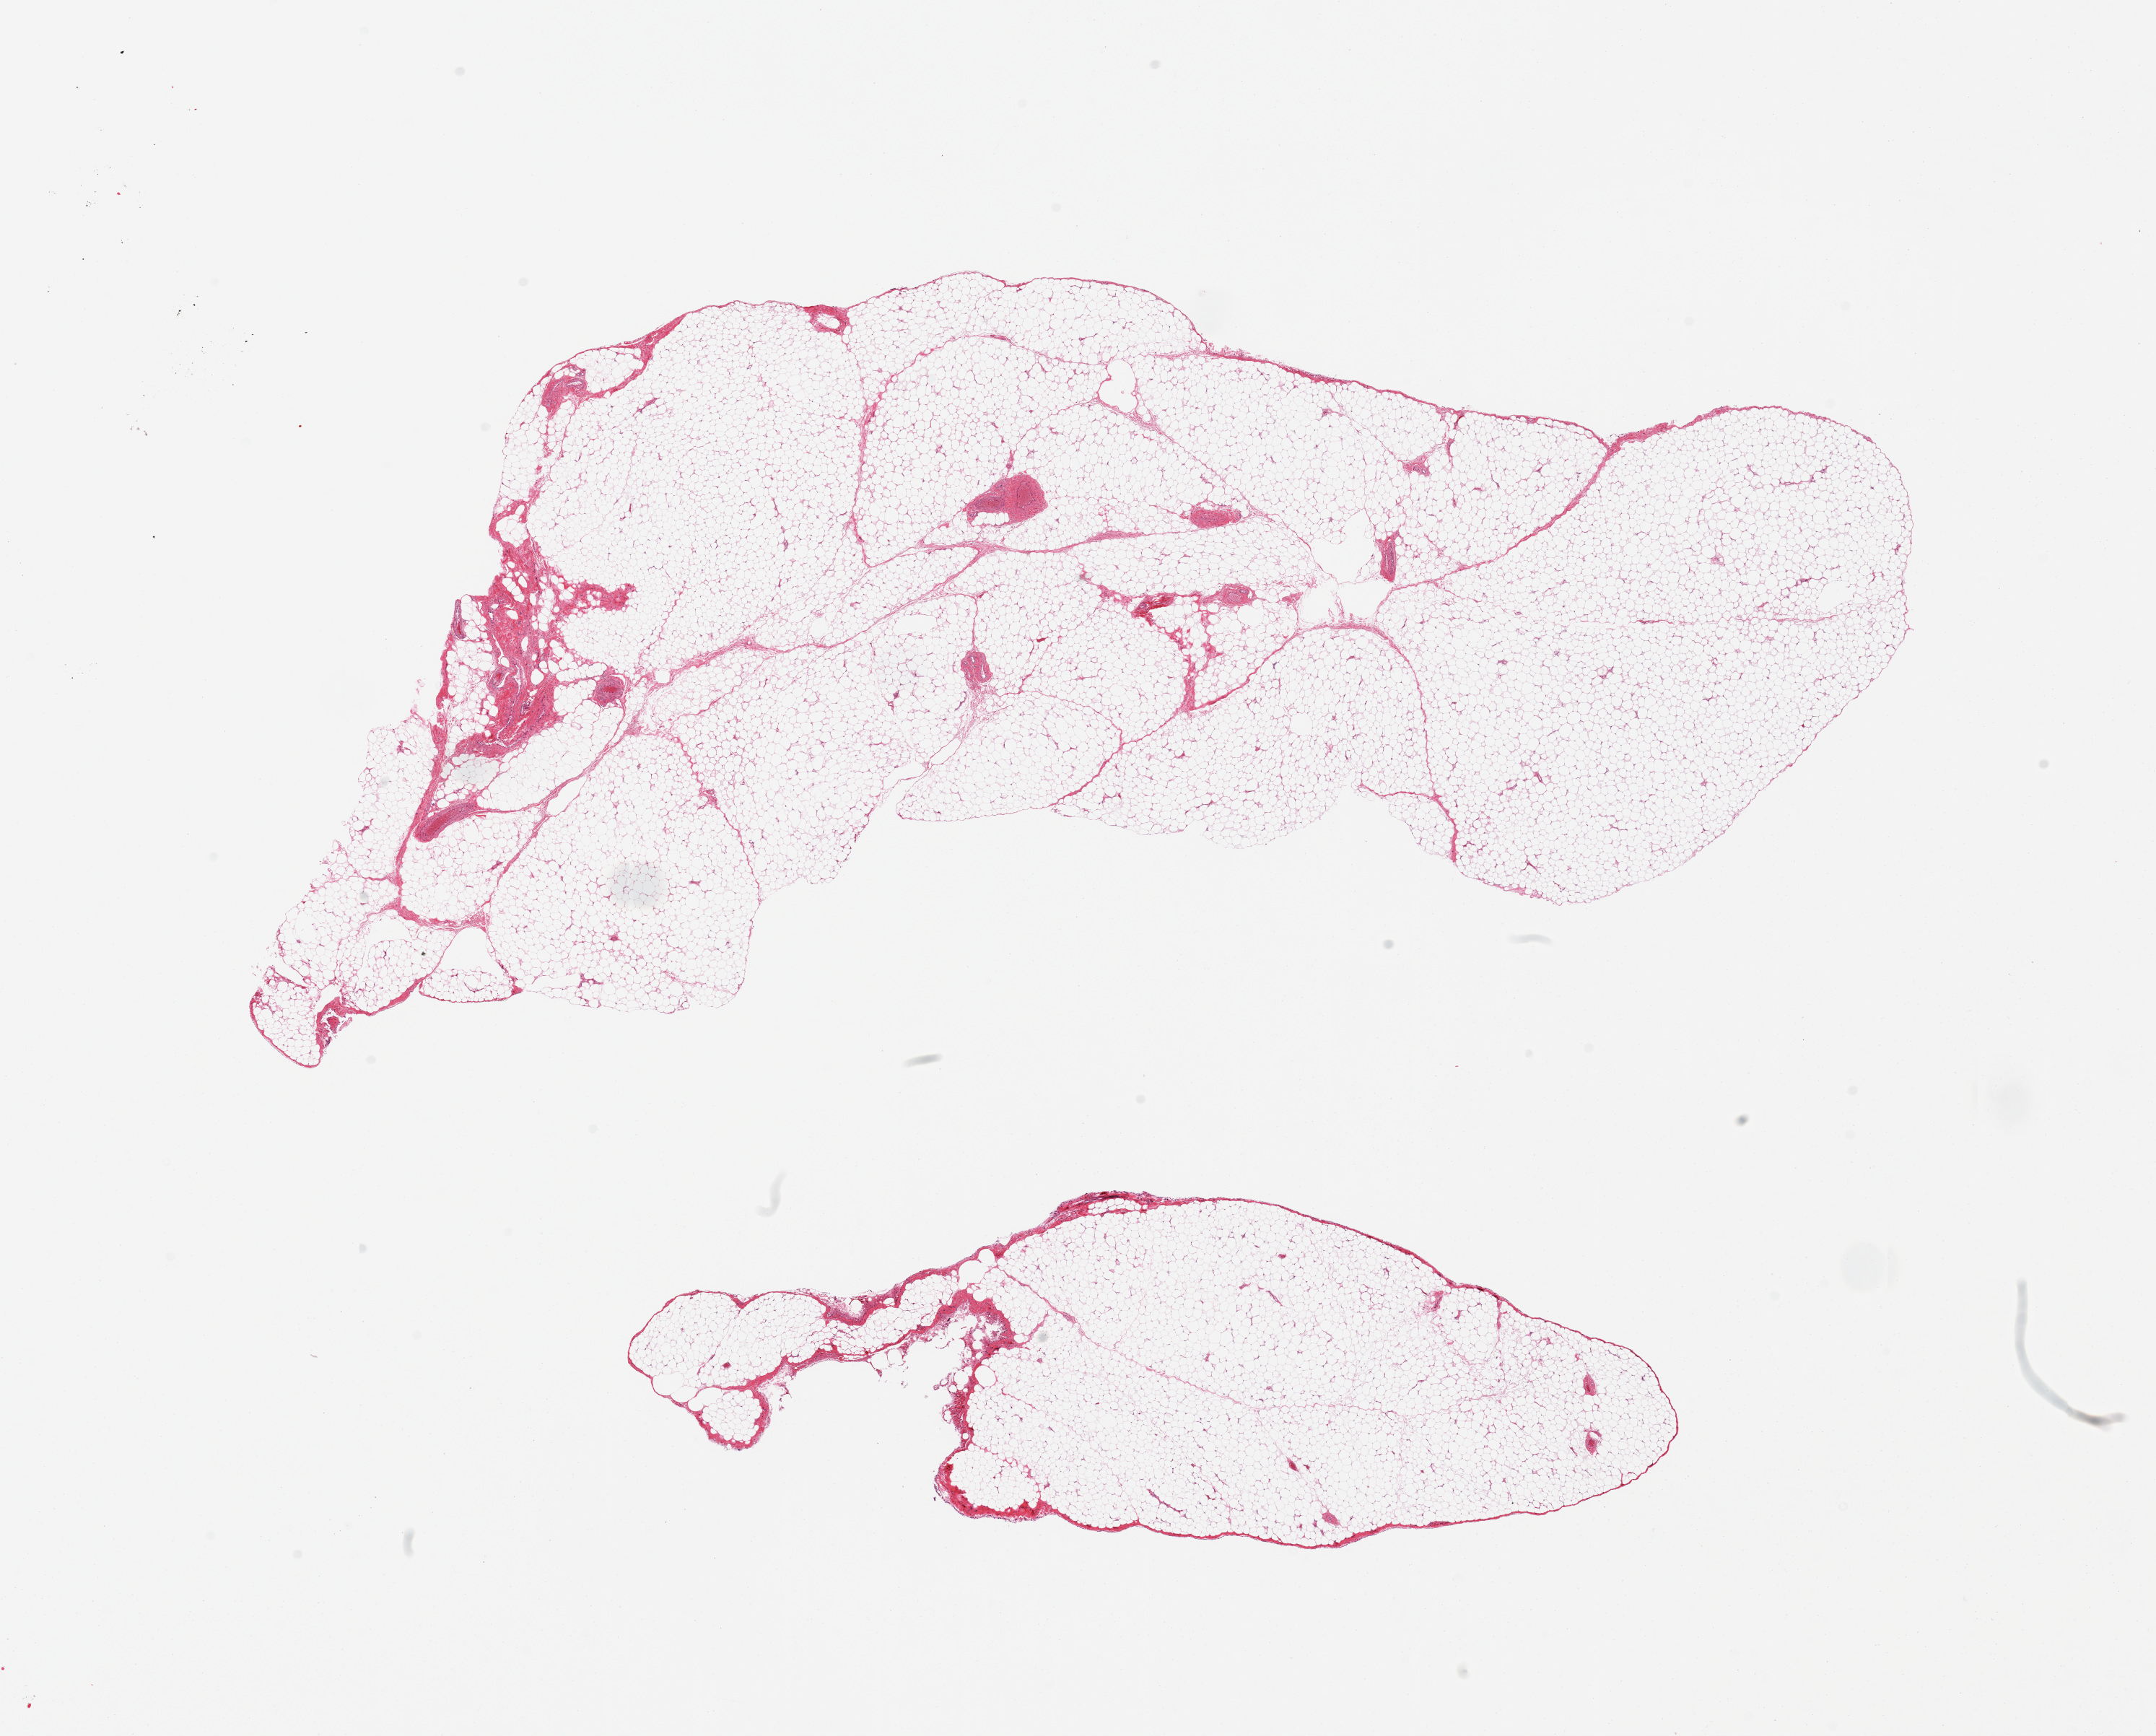
Whole-slide image, haematoxylin and eosin stain, brightfield — a low-resolution overview of the entire scanned area, about 23.6 x 19.0 mm; PAXgene-fixed, paraffin-embedded tissue; section of omentum (target tissue); tissue donor sample. Female donor.
Reviewer comment on this tissue sample: 2 pieces, ~5-10% fibrous/vascular tissue.